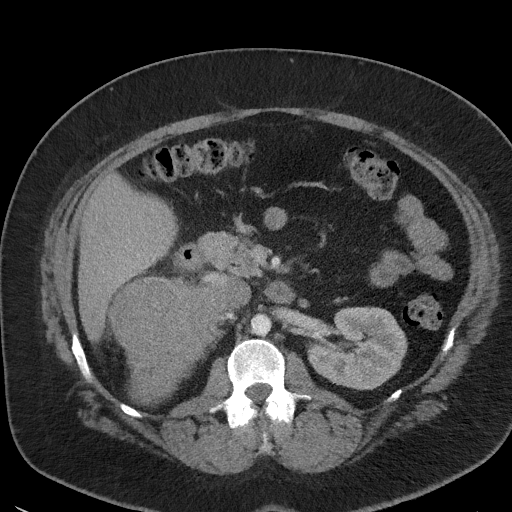
Contrast-enhanced abdominal CT, one axial slice; slice 23 of 56 in the series (ordered by position); reconstruction kernel I41f/3; intravenous contrast given; soft-tissue window (W 400 / L 40 HU); 5 mm slice thickness; 512 × 512 image matrix, field of view 373 × 373 mm. Female patient, age 35 years. Case-level facts recorded for this patient, not image findings: diagnosis: adrenocortical carcinoma; tumour side: right adrenal; tumour size at pathology: 15 cm.
Structures marked on this image (semi-automatically segmented with operator editing):
- mass: bounding box (x1, y1, x2, y2) in pixels: (113, 278, 227, 403)